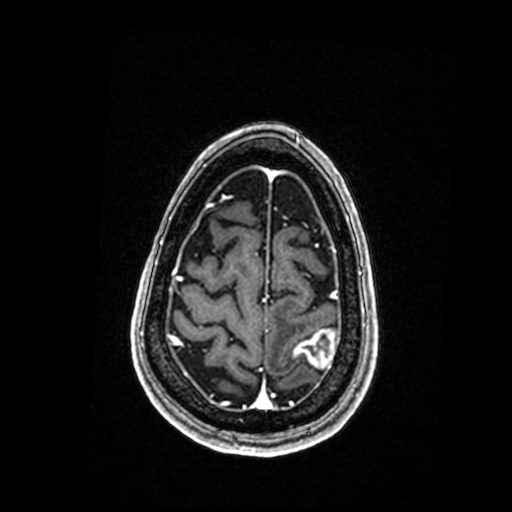
Brain MRI from a brain-tumour surgery series, one axial slice. Position 42 of 192 along the scan axis. T1-weighted post-contrast. 0.98 mm slice thickness. 512 × 512 image matrix, field of view 250 × 250 mm. Case-level facts recorded for this patient, not image findings: histopathology: Metastastic Carcinoma, Poorly Differentiated; tumour location: Left Parietal.
Annotated regions visible in this slice (manually delineated by an expert):
- tumour: box from (x=294, y=330) to (x=335, y=368) px